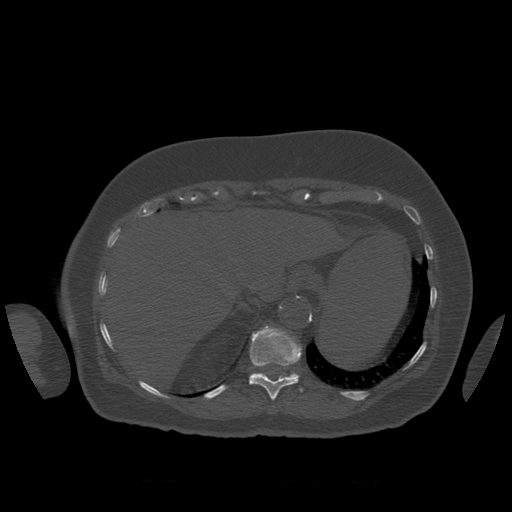
CT including the spine, one axial slice. 120 kVp. Bone window (W 1800 / L 400 HU). 1.25 mm slice thickness. 512 × 512 image matrix, field of view 404 × 404 mm. Patient age 81 years. From the clinical record (not read from this slice): primary cancer: renal; vertebrae with lytic lesions (as recorded): L1.
Outlined on this slice (semi-automatic segmentation, software-assisted and operator-edited):
- T11 vertebra: bounding box [x1, y1, x2, y2] px = [249, 326, 303, 400]
- T12 vertebra: [283, 373, 299, 378]